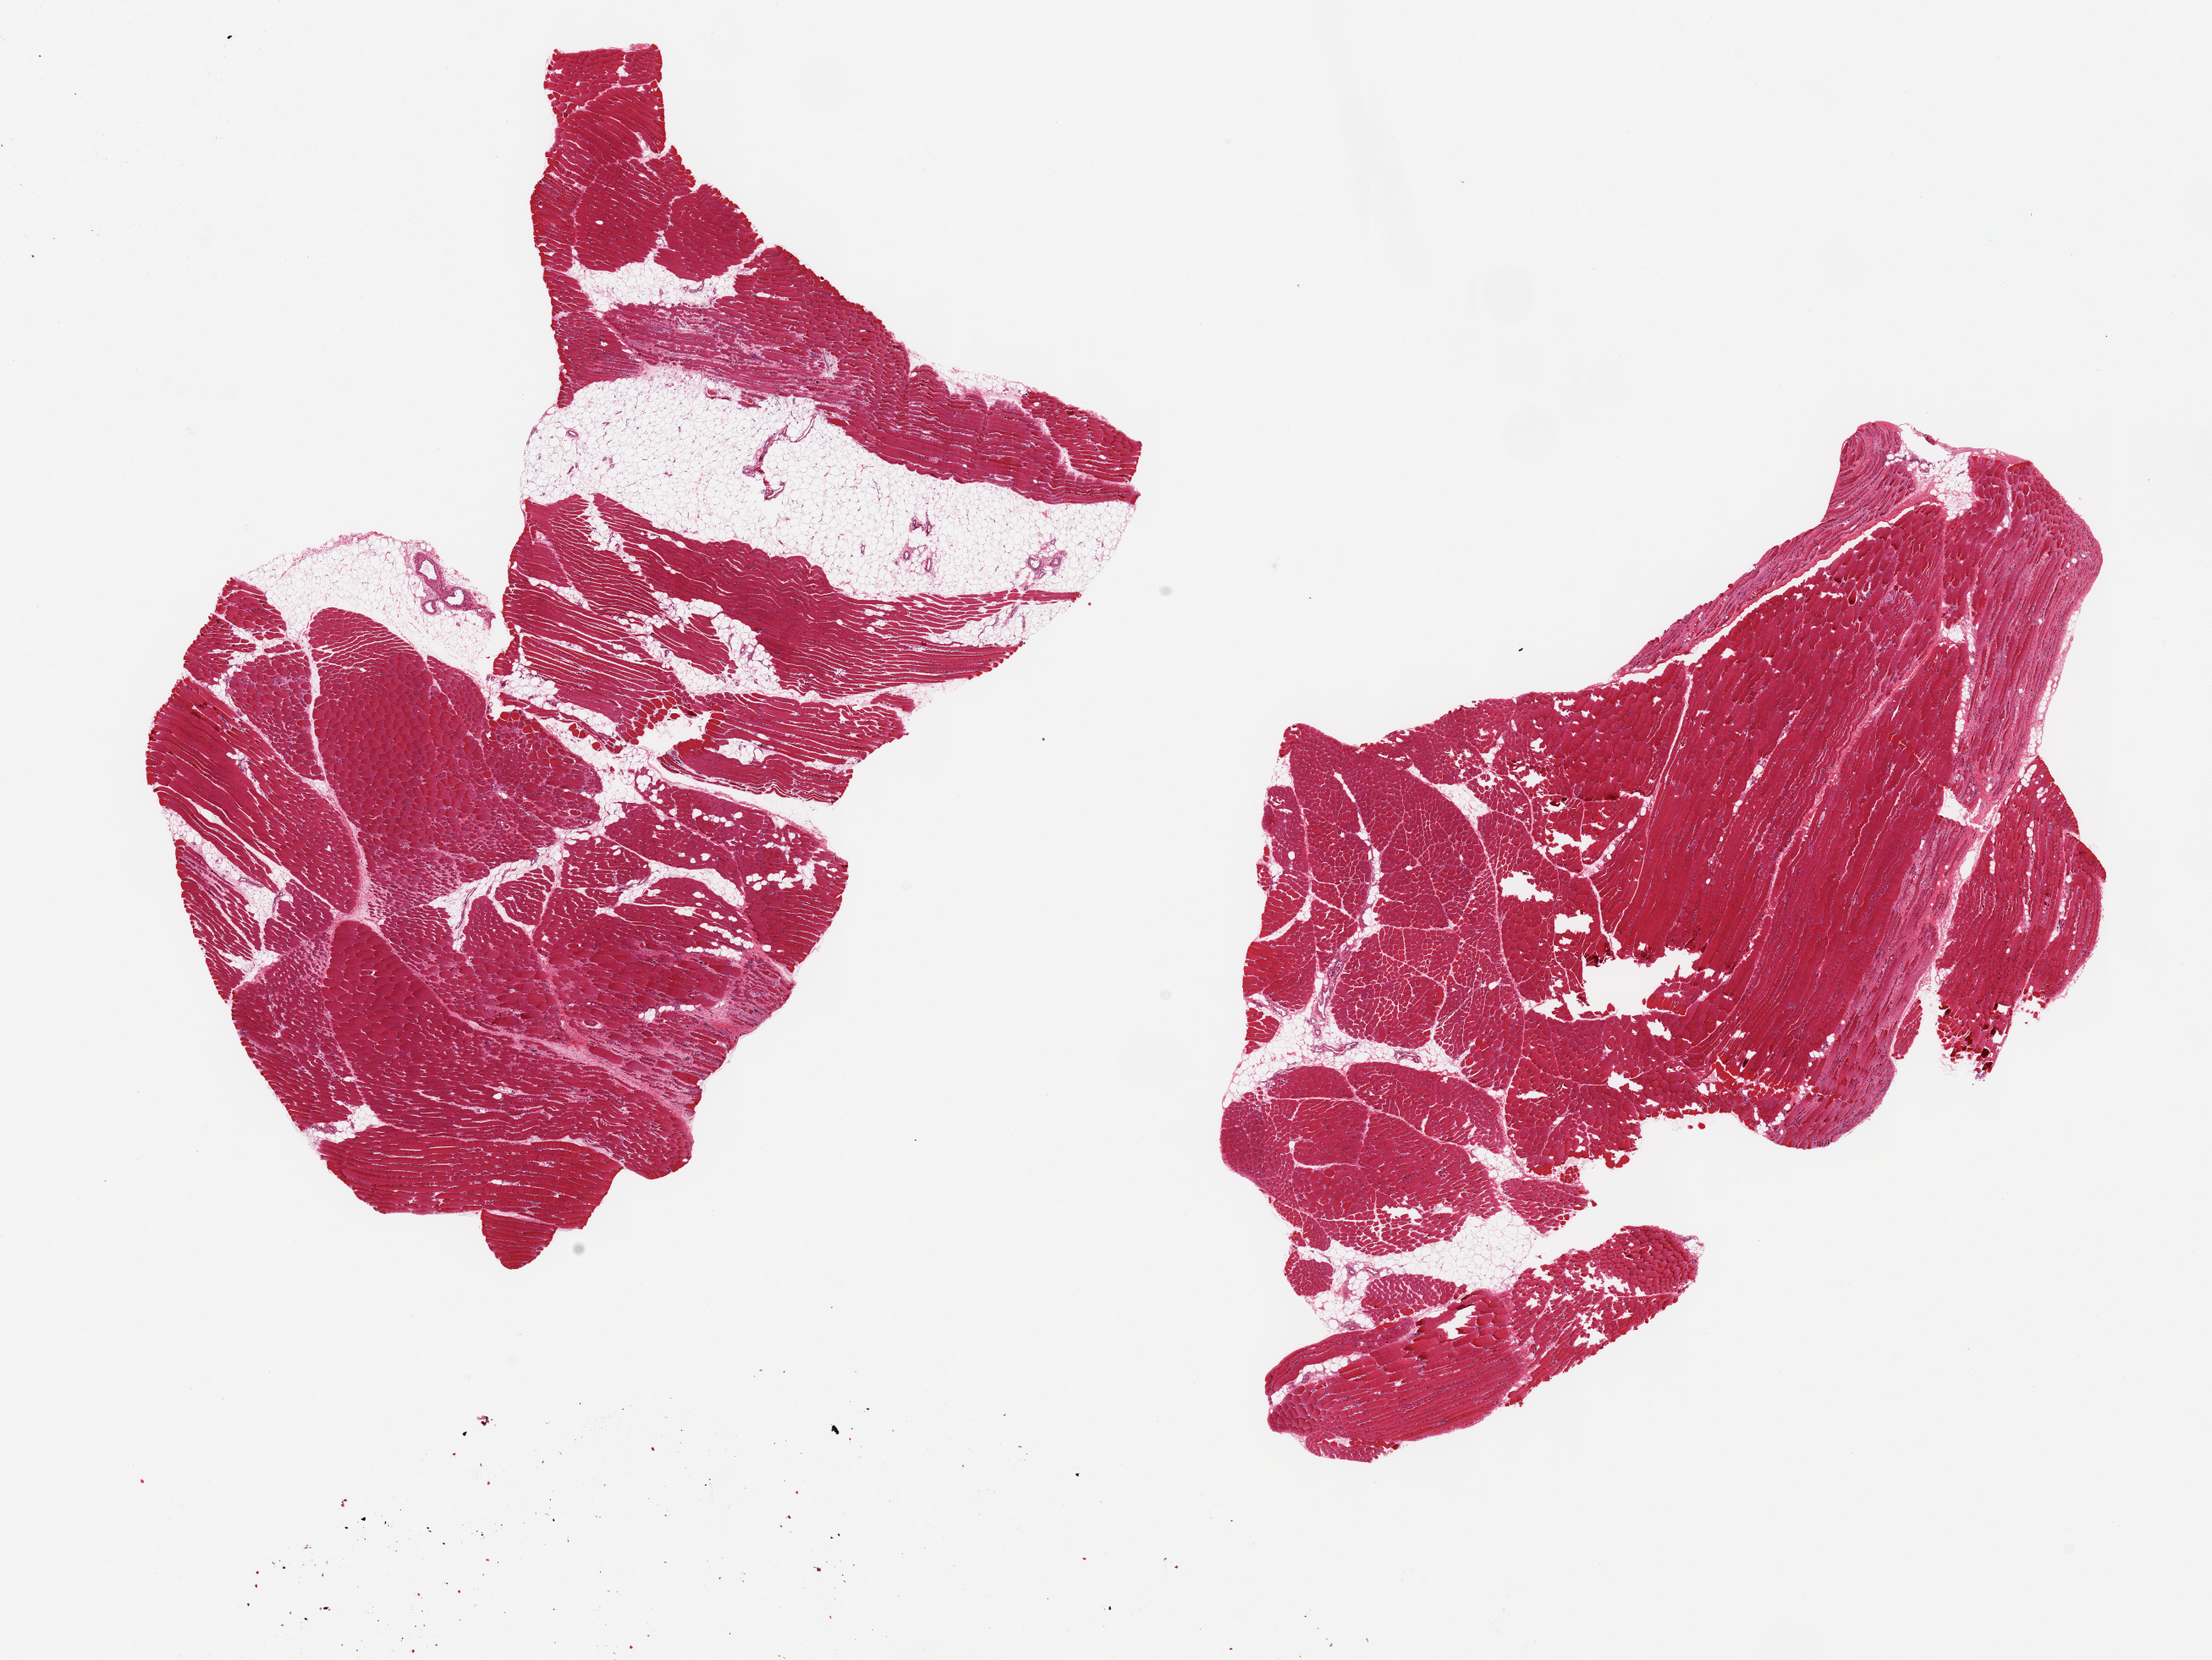
Digitized hematoxylin and eosin (H&E)-stained section — a low-resolution overview of the entire scanned area, about 20.7 x 15.5 mm. PAXgene-fixed paraffin-embedded (PFPE) section. Target tissue: skeletal muscle. Tissue donor sample. Donor sex: female.
• review note (as recorded): 2 ~10x6mm aliquots, ~ 20% interstitial fat. Focal areas of scarring